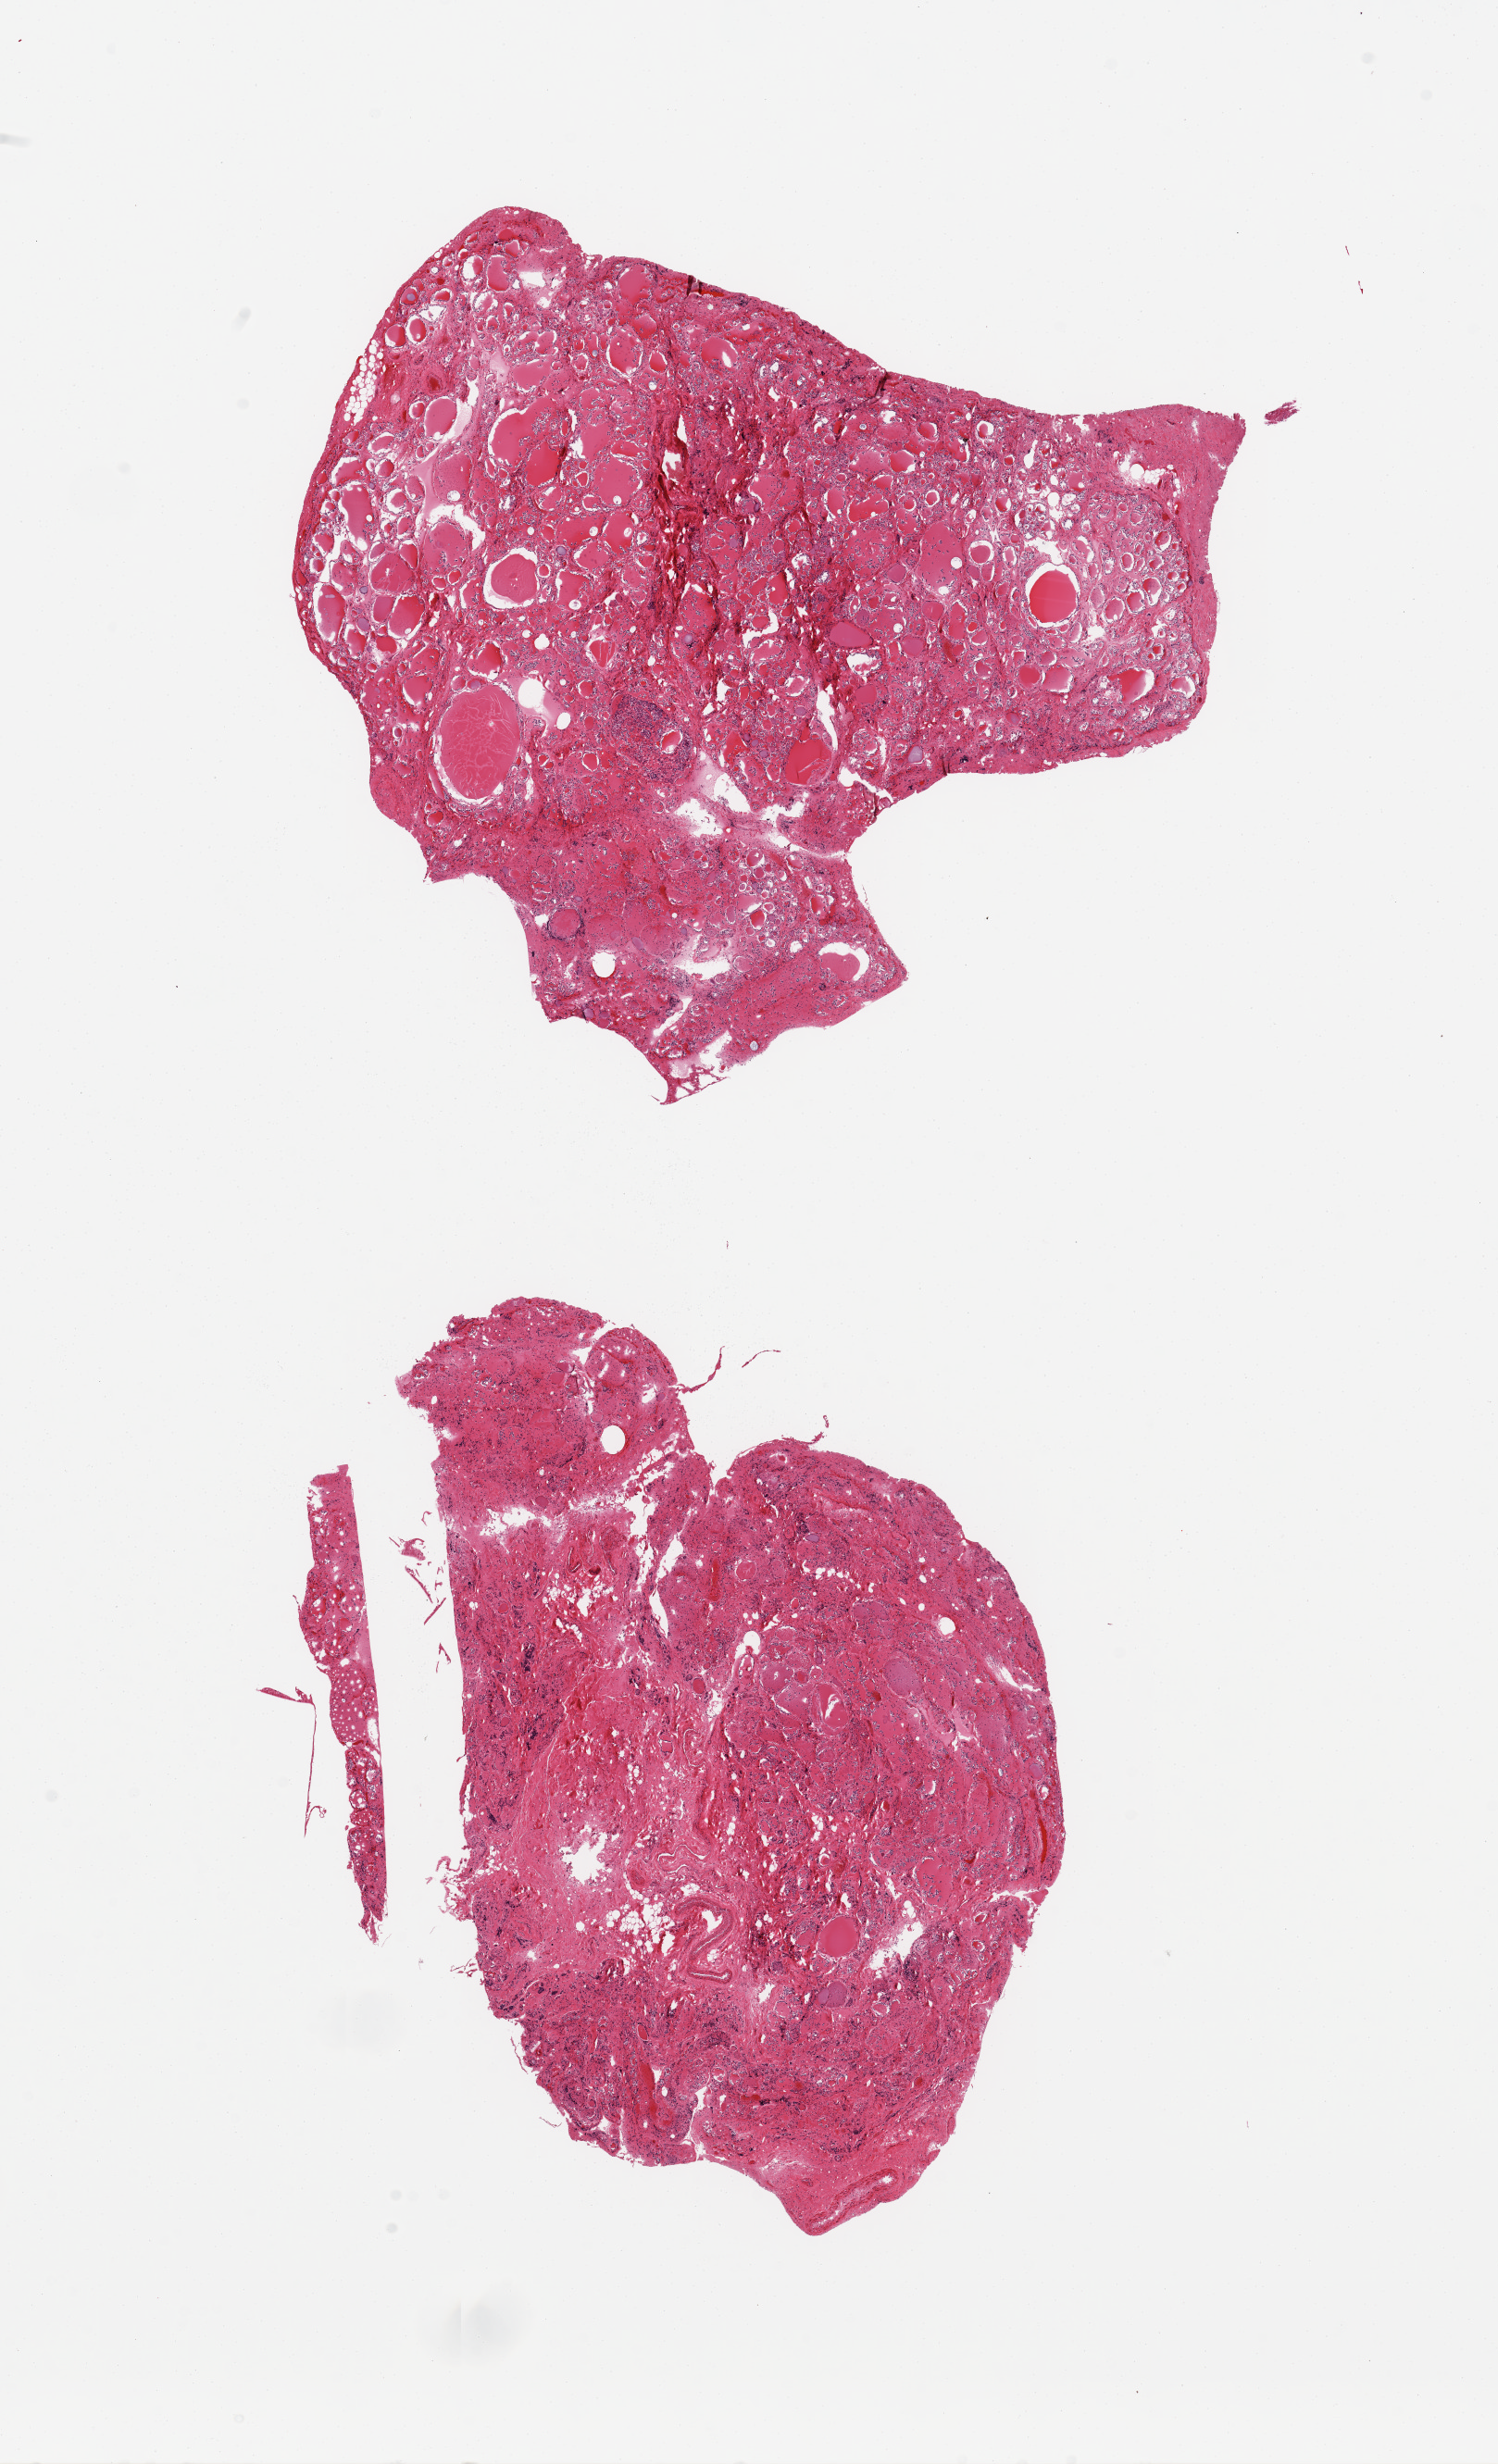
Whole-slide image, hematoxylin and eosin (H&E) stain, low-resolution overview of the scanned area, about 12.8 x 21.1 mm (acquisition: 20x scan); PAXgene-fixed paraffin-embedded (PFPE) section; section of thyroid (target tissue); donor tissue sample. Donor sex: male.
Review note (as recorded): 2 pieces; fibrosis and hyalinization, multinodular, moderate to severe autolysis.